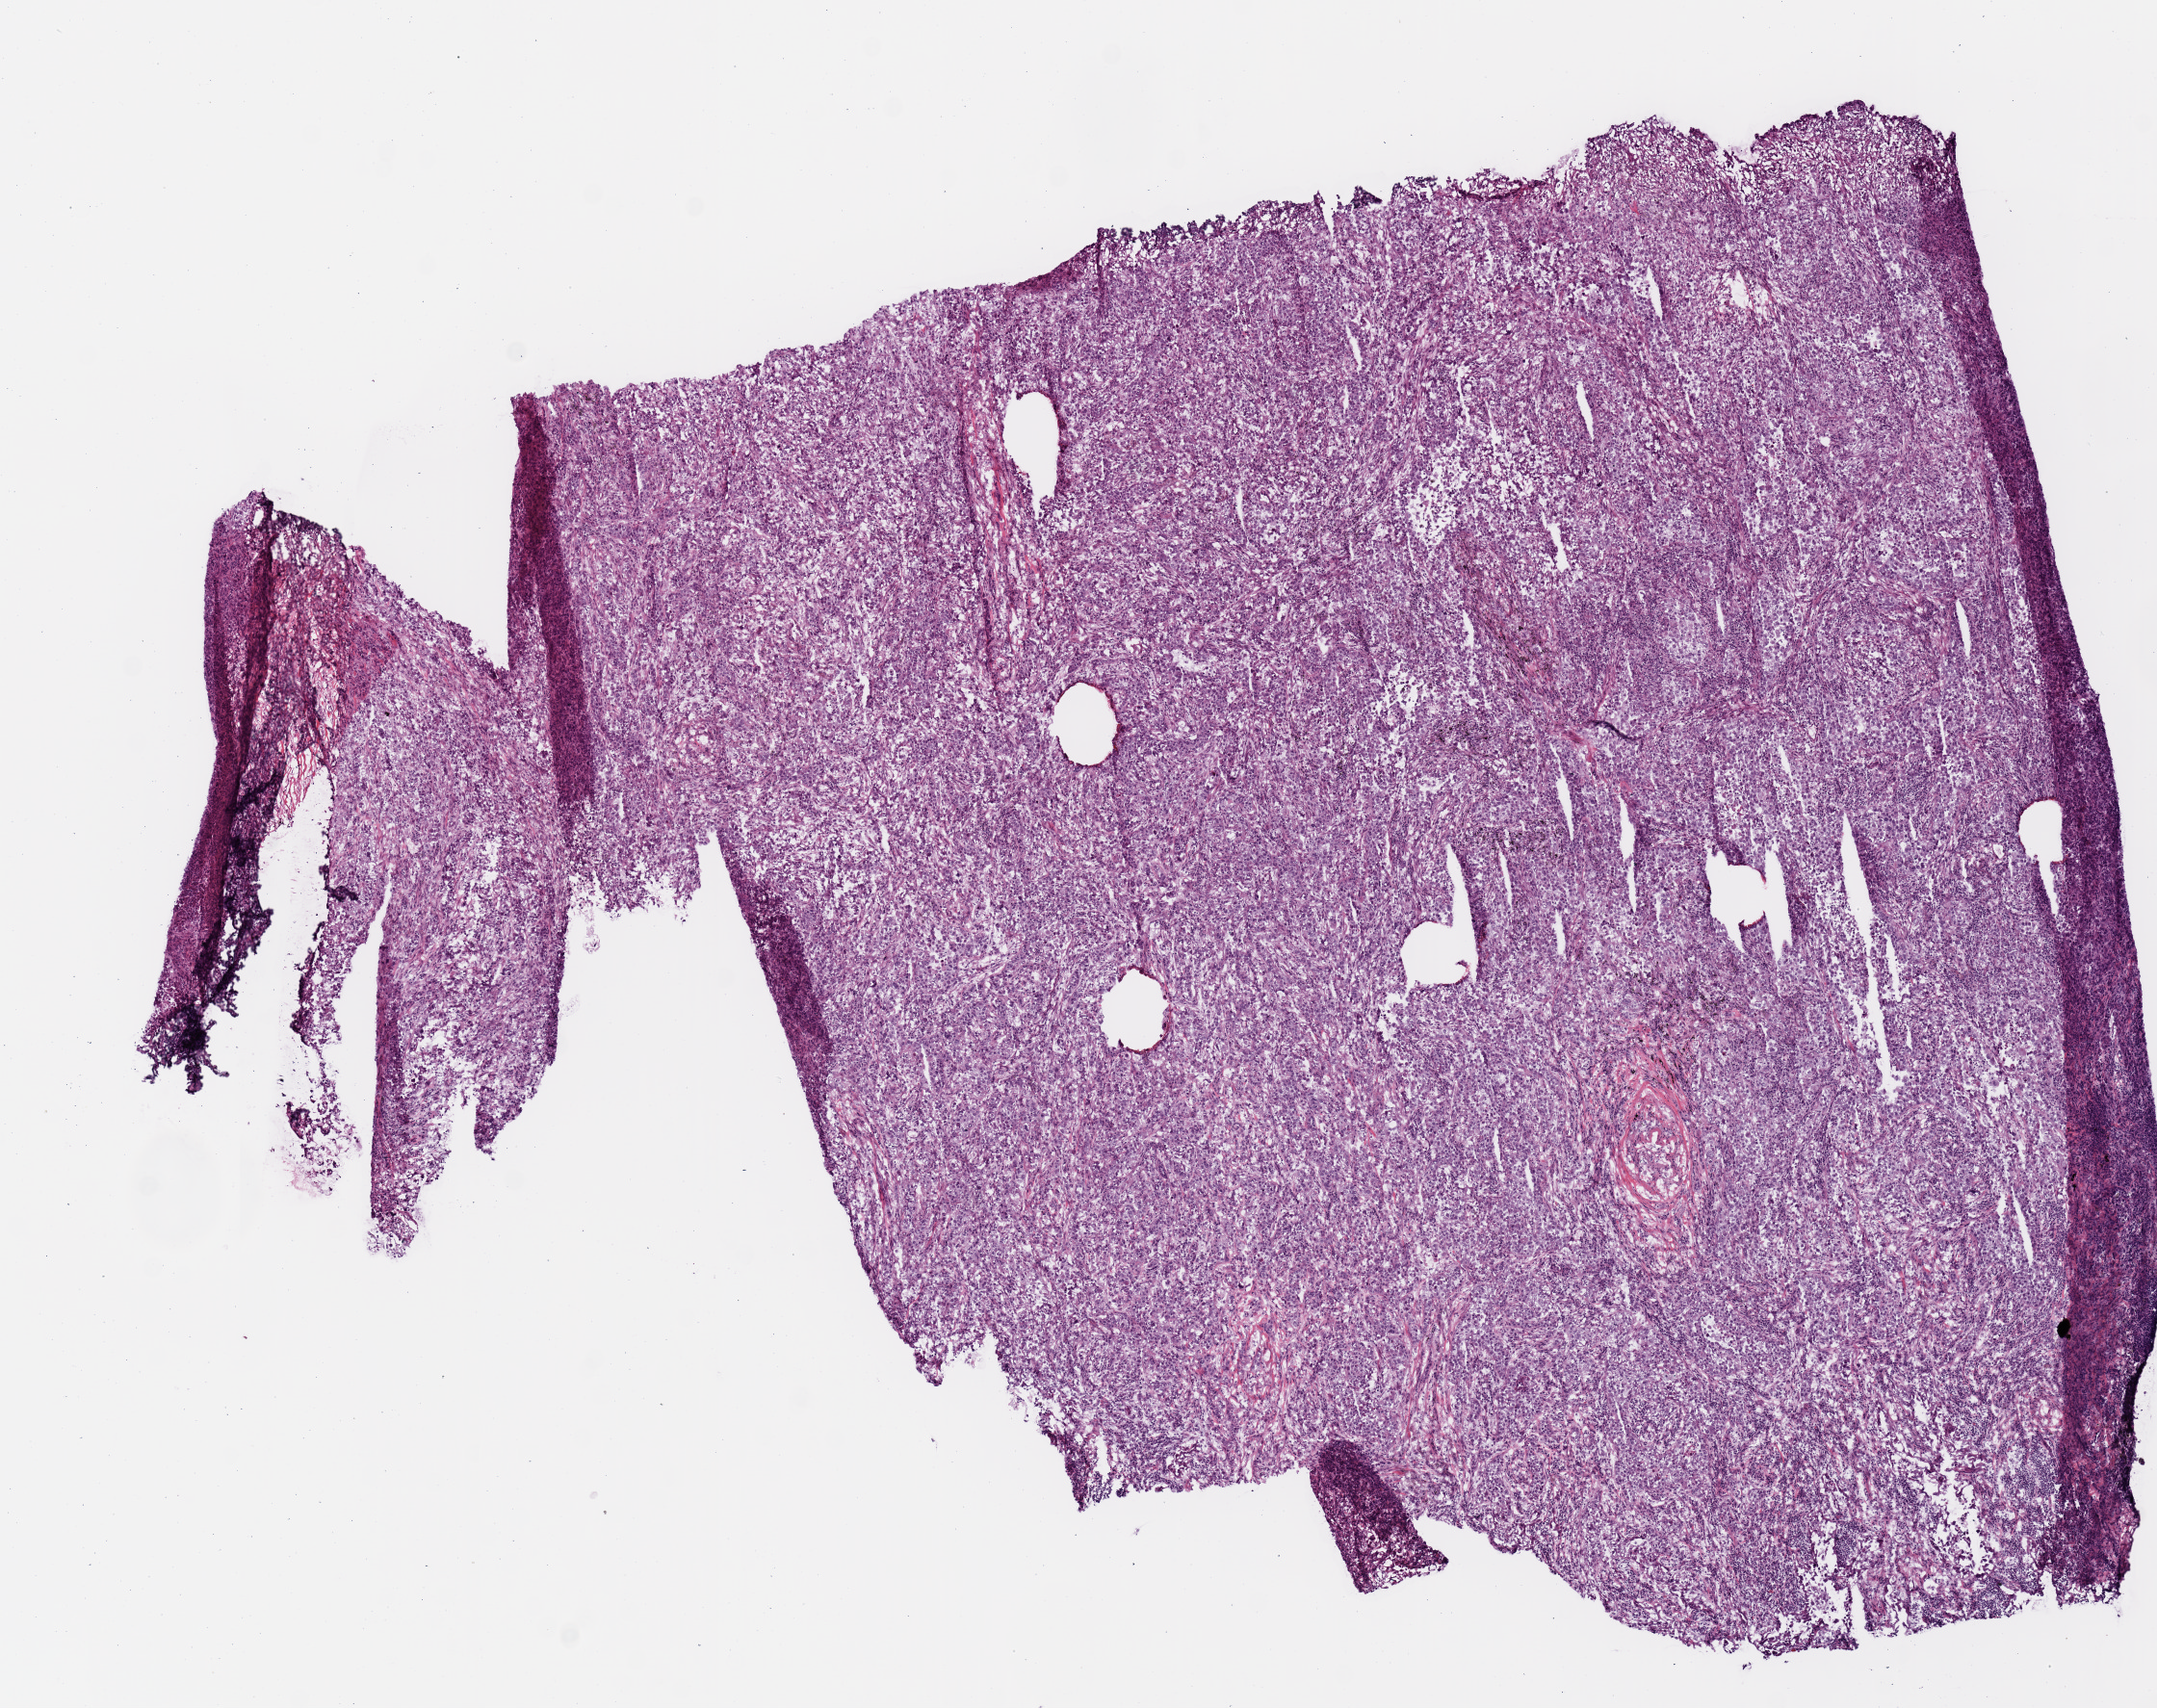
H&E whole-slide image, a low-resolution overview of the entire scanned area, about 8.9 x 7.0 mm (acquisition: 20x scan). Frozen section from the top of the tissue portion. Primary tumour sample from the lung. Female patient; age at initial diagnosis 73 years. Composition of this section per pathologist review: tumour nuclei 75%, necrosis 0%.
Histologic diagnosis: Adenocarcinoma, NOS (upper lobe, lung). AJCC pathologic stage: IB (7th edition). Laterality: right.